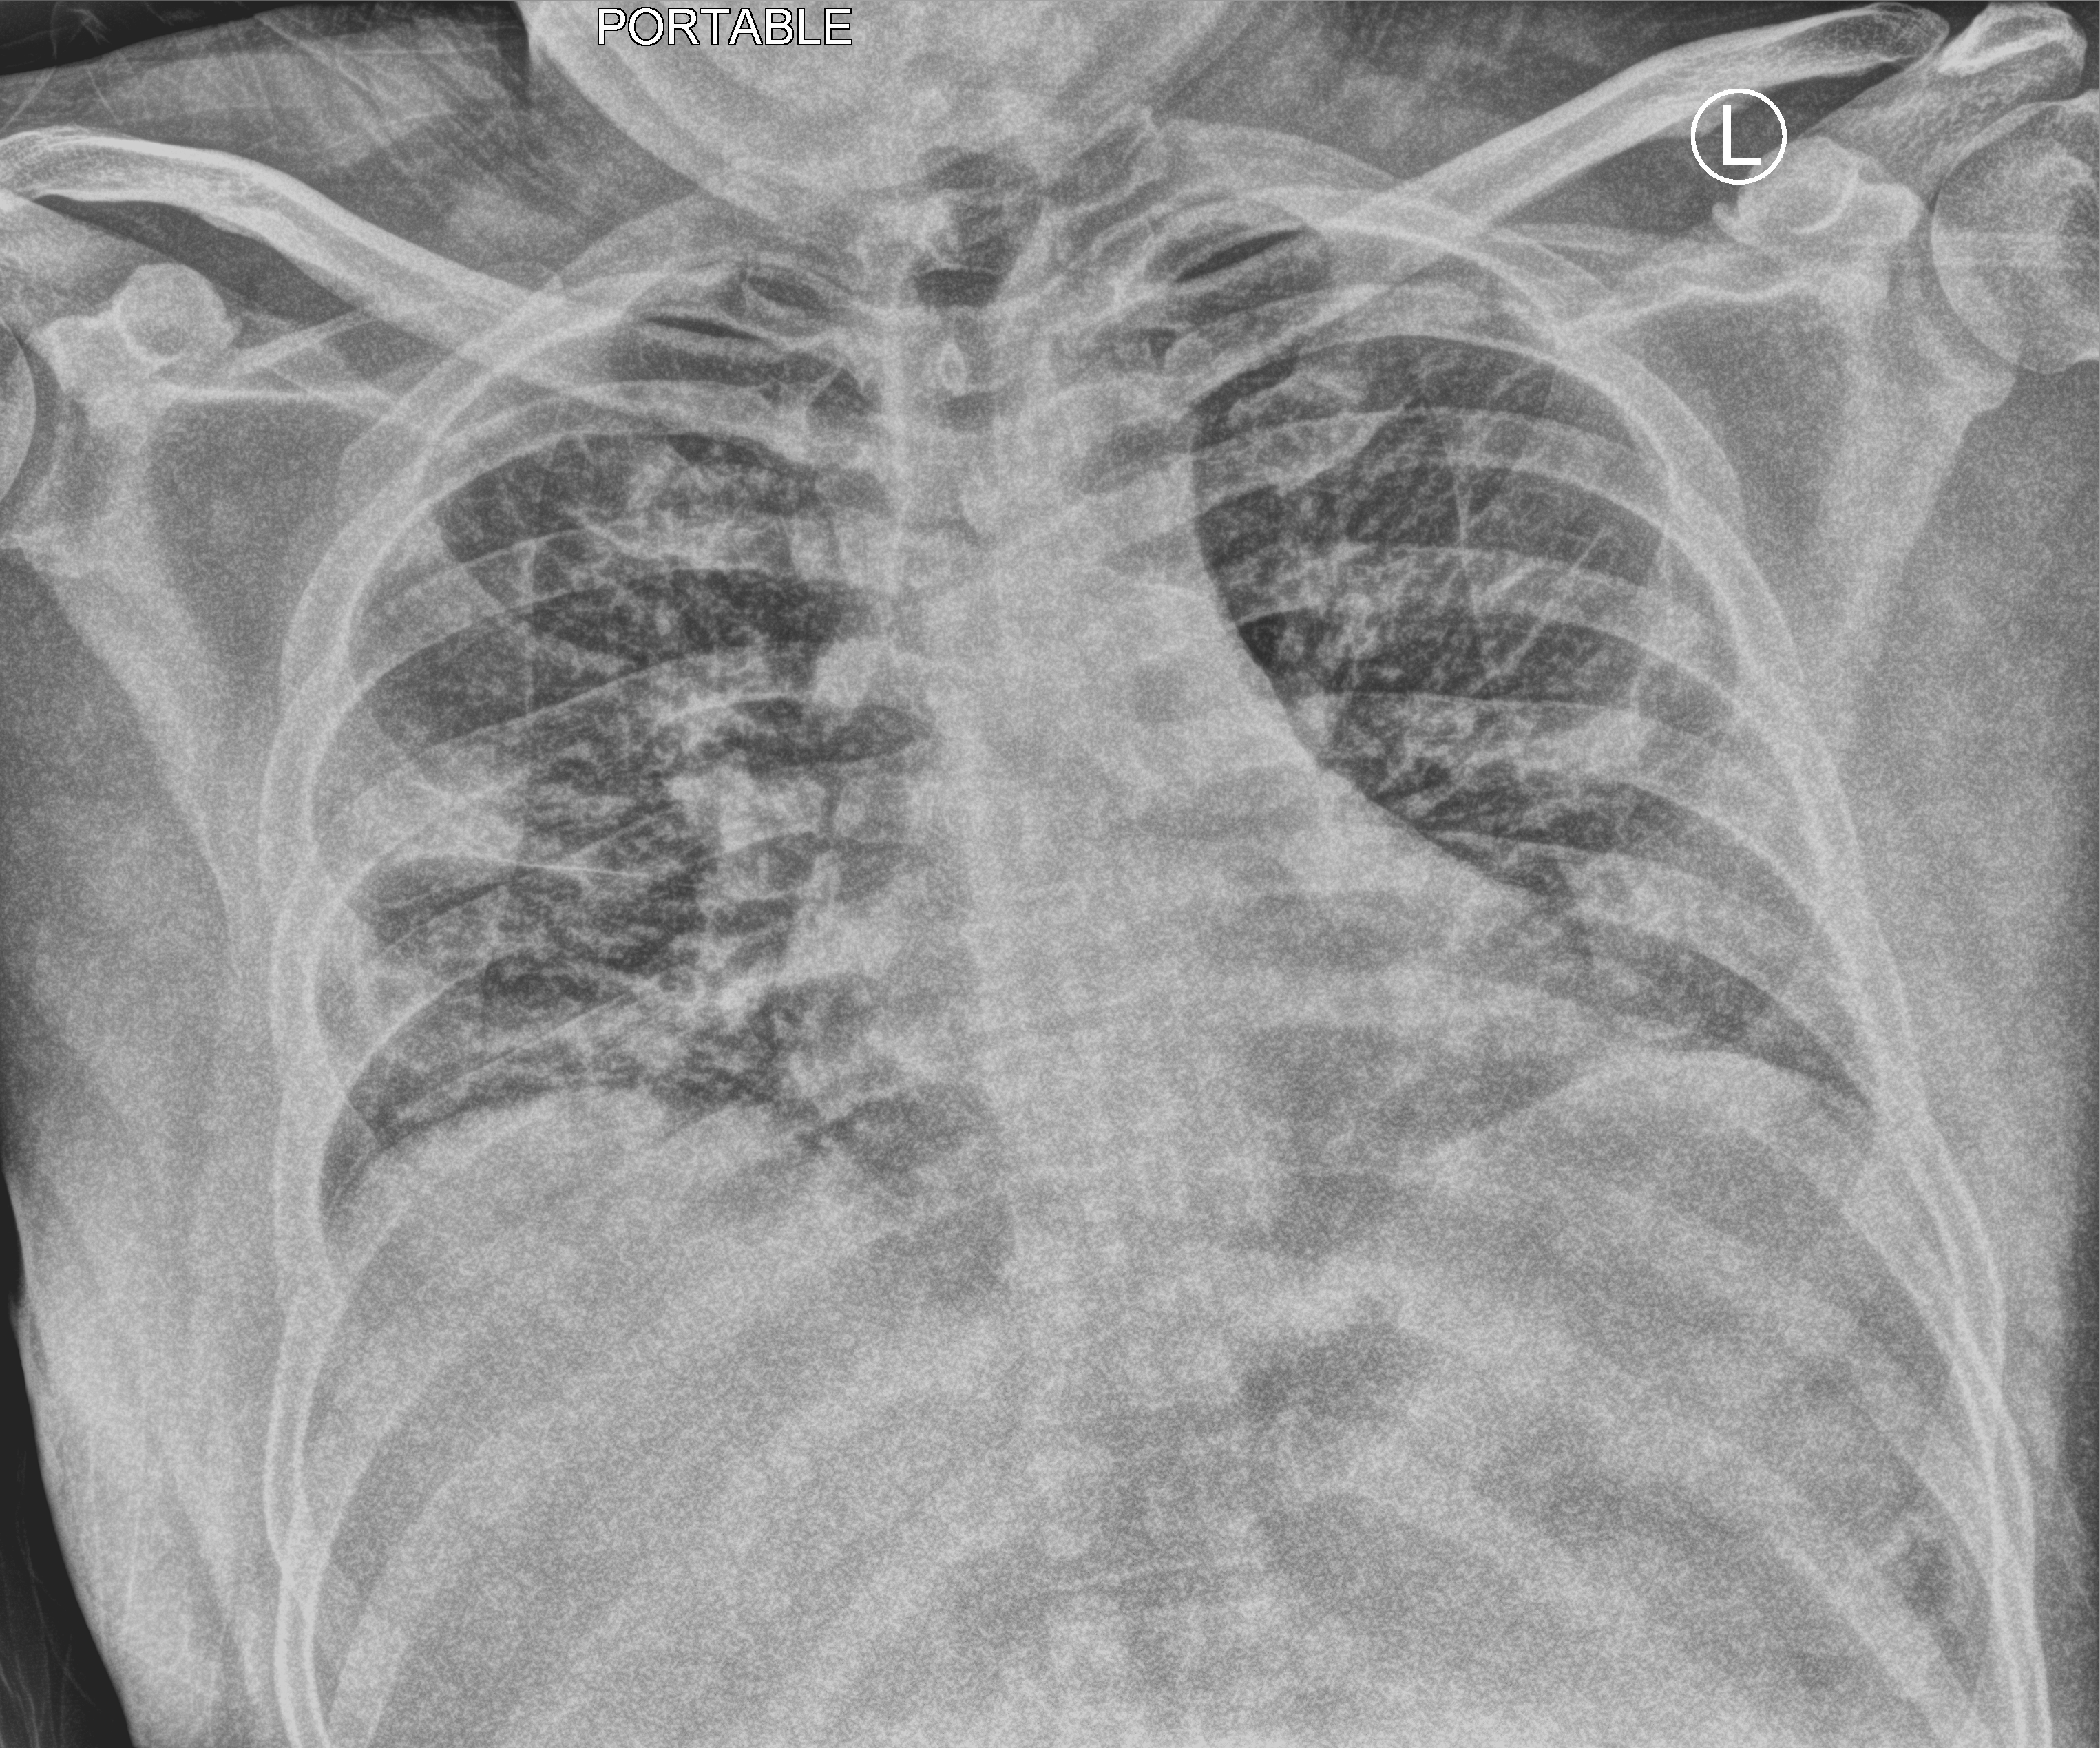
Chest X-ray (portable); anteroposterior (AP) projection. Male patient hospitalised with COVID-19, age 18–59 years.
From the hospital-stay record, not from the radiograph (when in the stay this image was taken is not recorded): admitted to intensive care during this hospital stay: no; mechanically ventilated during this hospital stay: no.